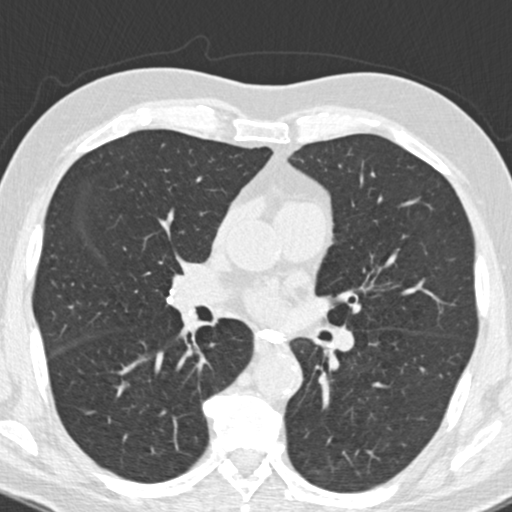
Axial slice from a low-dose chest CT screening exam. Second screening round (one year after baseline). Lung window (W 1500 / L -600 HU). Slice 85 of 177 in the series. Male, age 66 years at enrolment. Current smoker at enrolment.
Expert-annotated lung lesion, bounding box <182,305,211,342> (left, top, right, bottom; pixels). Screening reader's record for this exam (one nodule recorded; not confirmed to be the boxed lesion): non-calcified nodule or mass ≥4 mm, right upper lobe, 5 × 4 mm, smooth margins, pre-existing on the prior screen: yes; interval growth: no. Participant outcome: lung cancer diagnosed 403 days after this screen — squamous cell carcinoma, NOS, right lower lobe, poorly differentiated (G3), stage IIA (AJCC 6th edition), 22 mm at pathology.